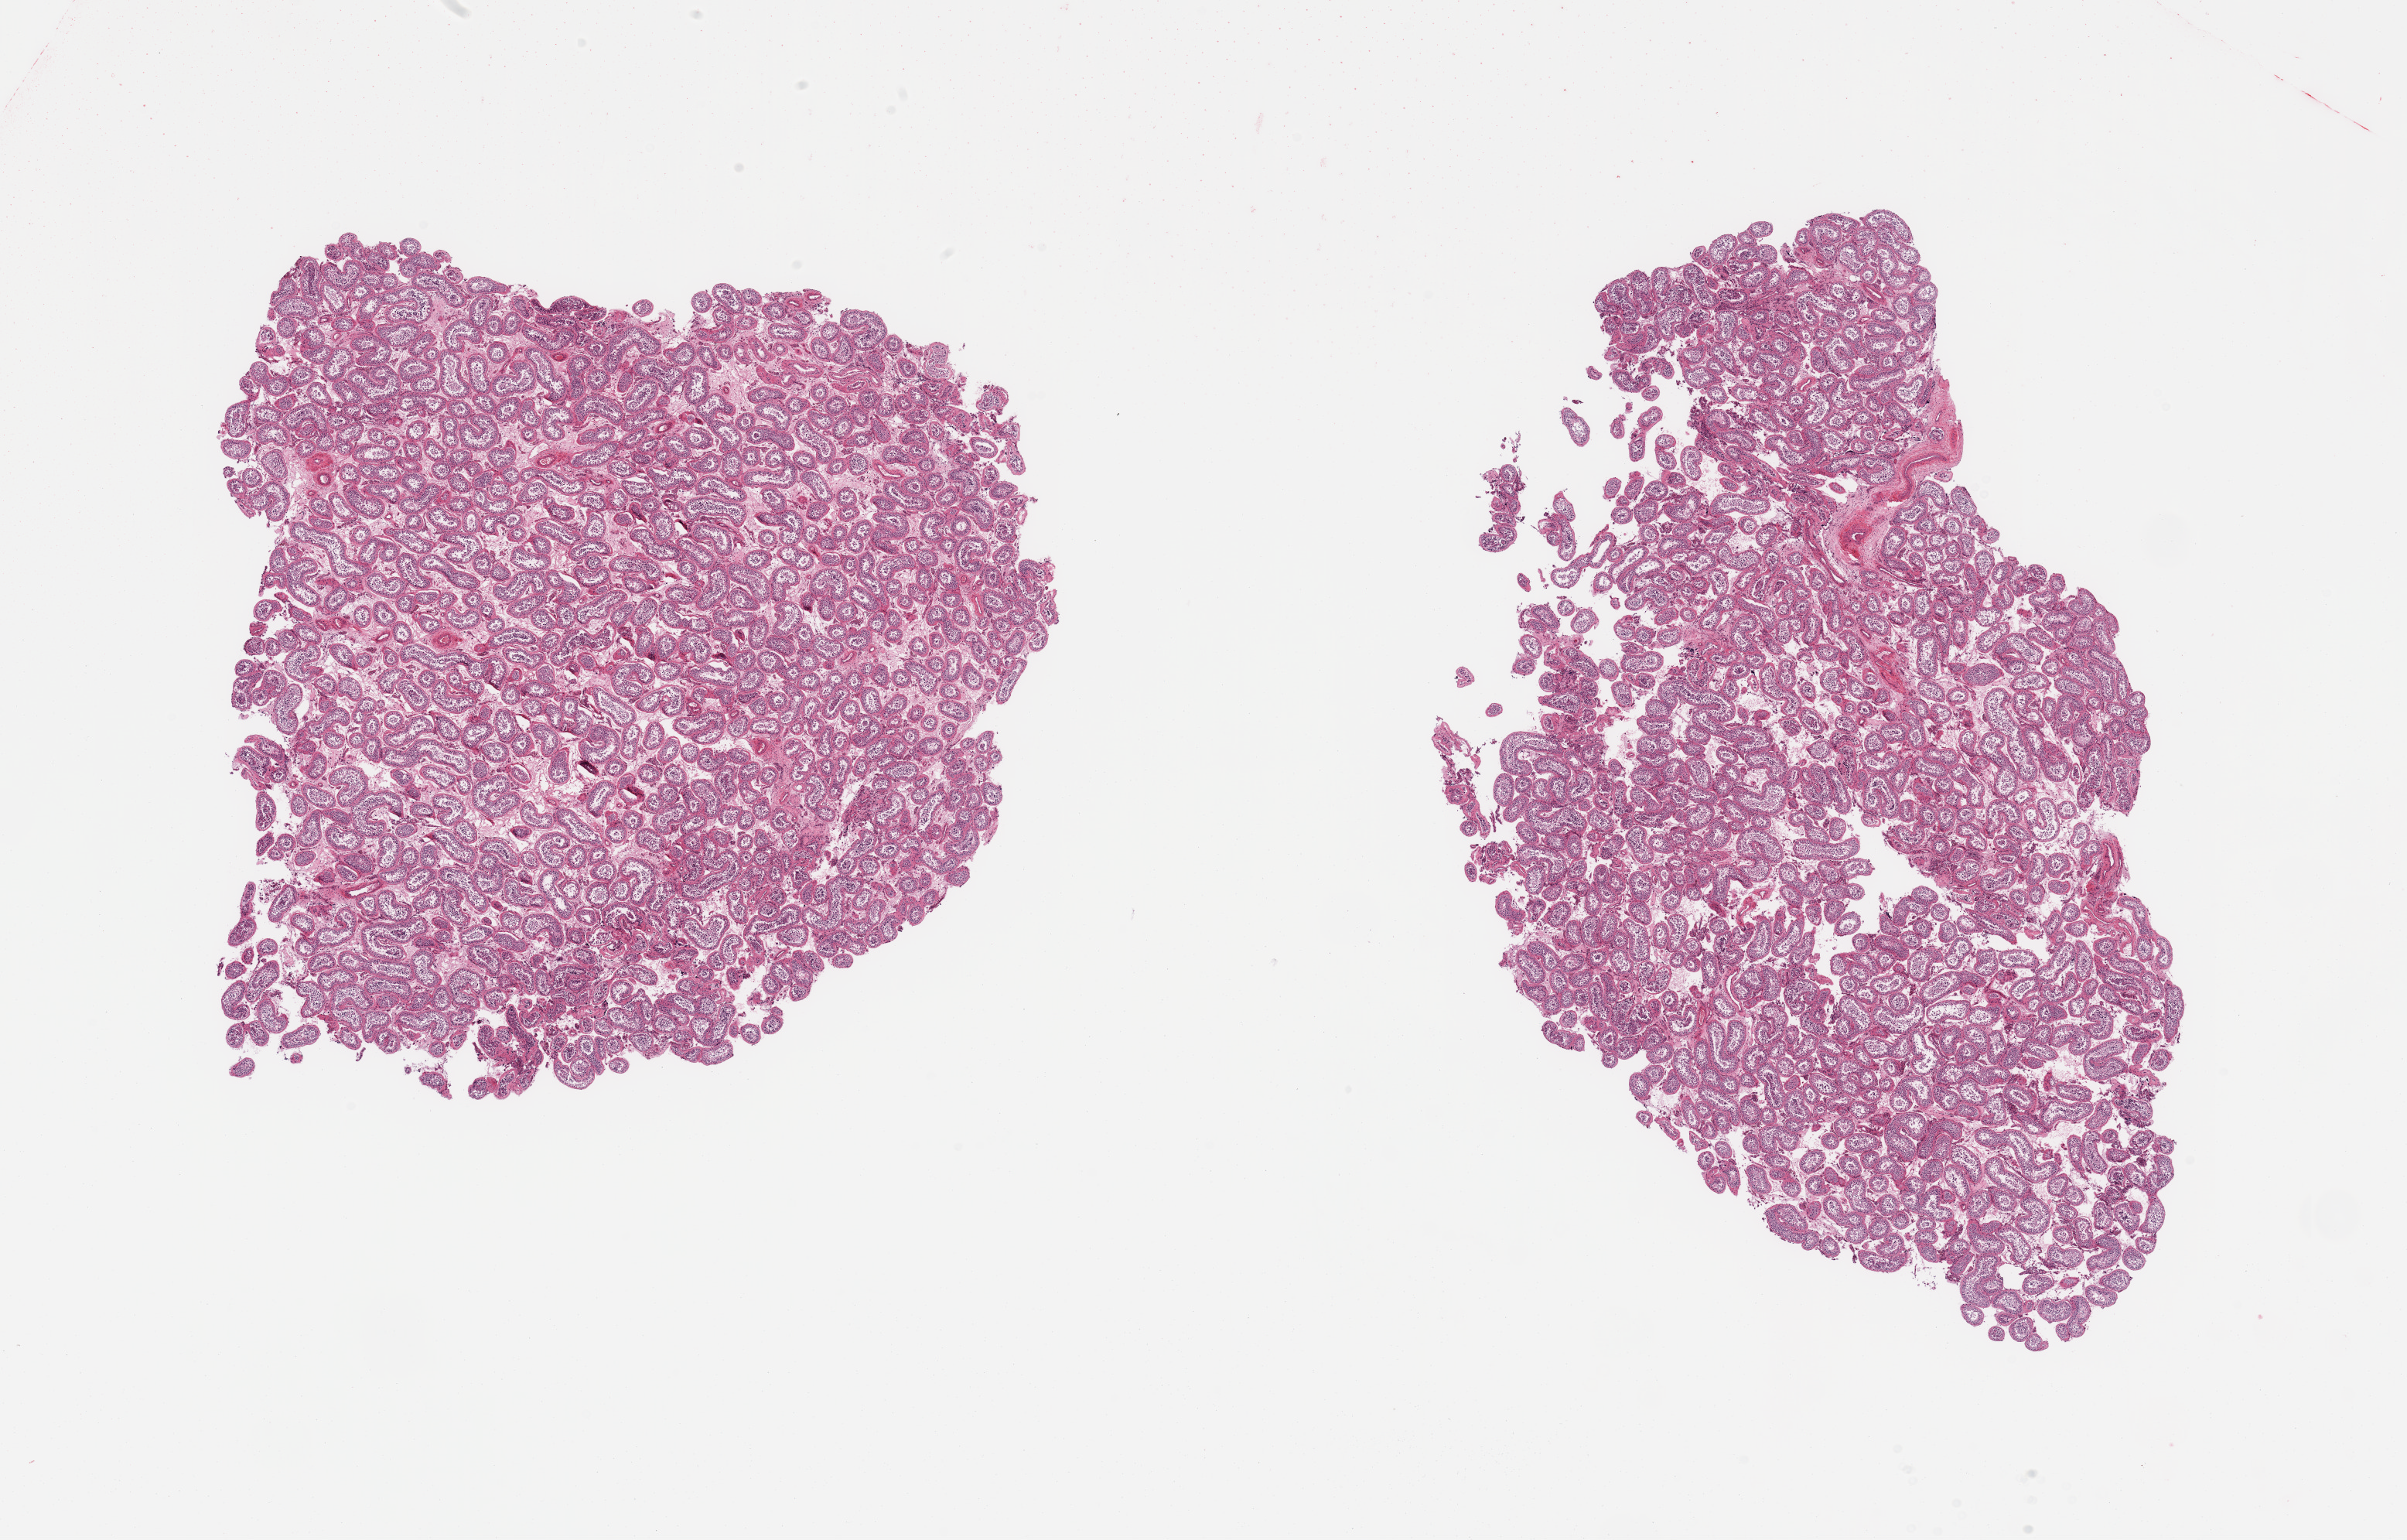
Whole-slide image, H&E stain, low-resolution overview of the scanned area, about 24.6 x 15.7 mm; PAXgene-fixed paraffin-embedded (PFPE) section; sampled site (target tissue): testis; donor tissue sample.
Review note (as recorded): 2 pieces, spermatogenesis present; appears reduced.